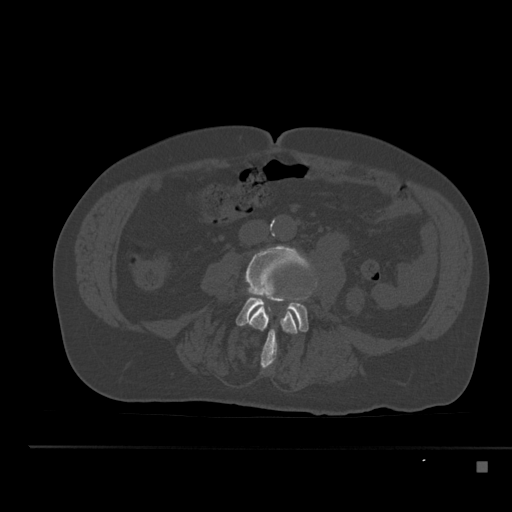
CT including the spine, one axial slice. Position 153 of 517 along the scan axis. 120 kVp. Bone window (W 1800 / L 400 HU). 1.5 mm slice thickness. 512 × 512 image matrix, field of view 408 × 408 mm. Male patient, age 70 years. From the clinical record (not read from this slice): primary cancer: renal; vertebrae with lytic lesions (as recorded): T4, T6, T10, T12, L3, L4, L5.
Outlined on this slice (semi-automatically segmented with operator editing):
- L3 vertebra: bounding box <246,246,317,369> (left, top, right, bottom; pixels)
- L4 vertebra: <236,295,309,332>